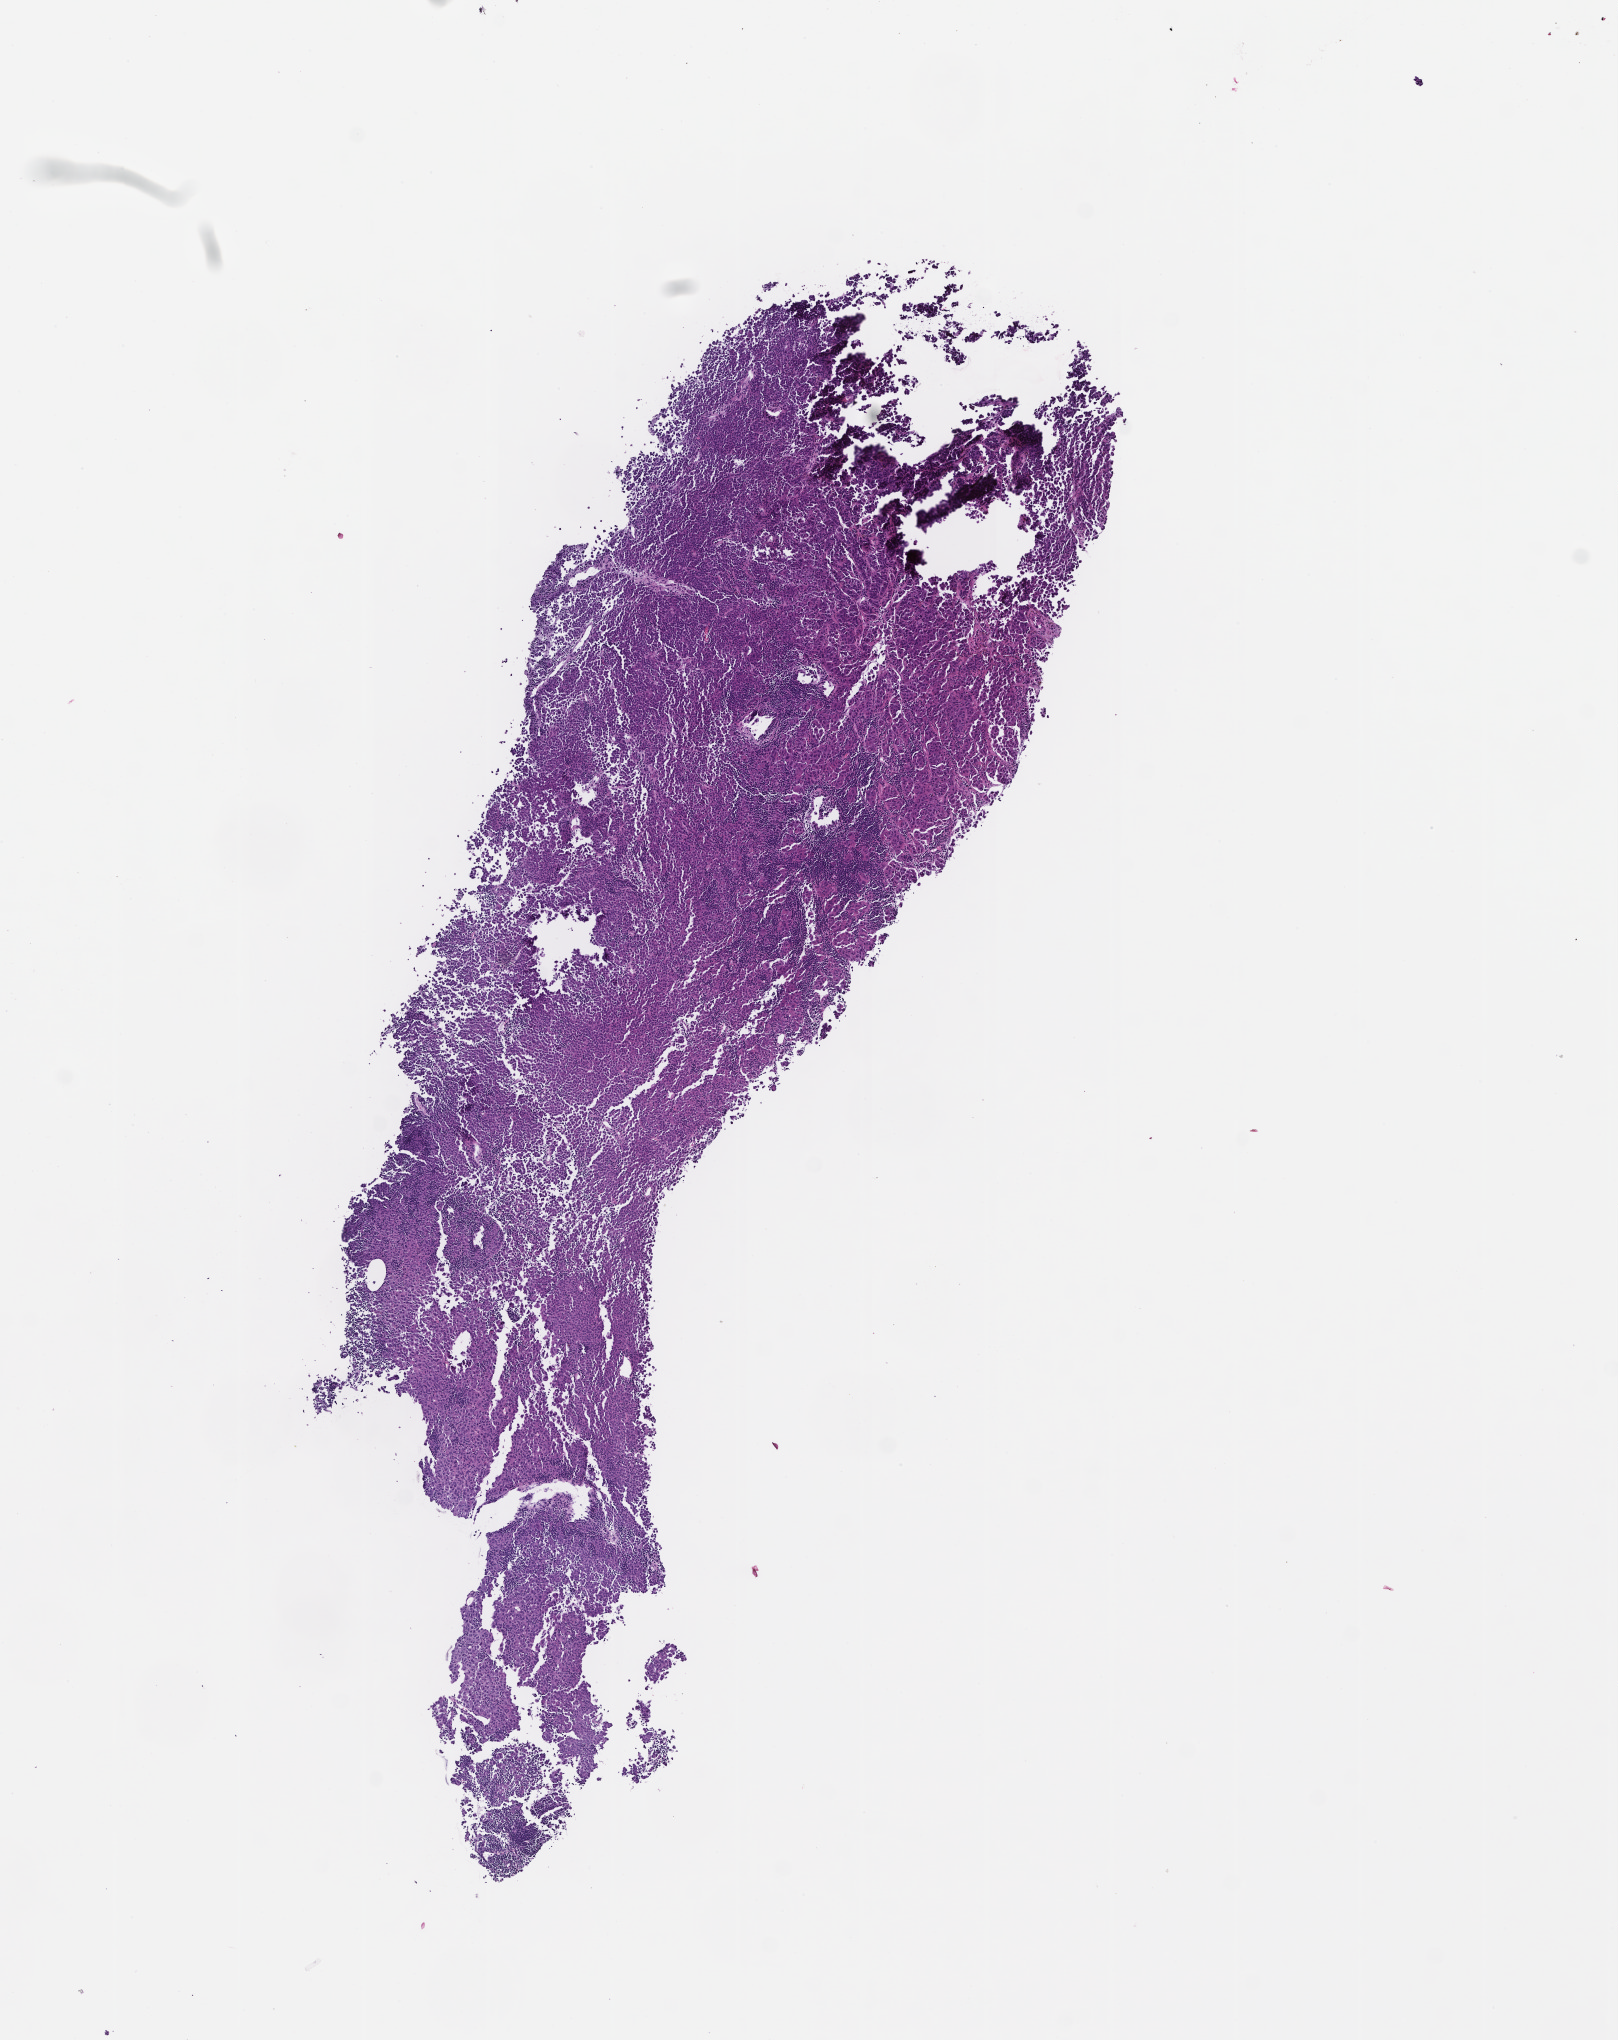
Haematoxylin and eosin whole-slide image, whole scanned area (about 6.5 x 8.2 mm) shown as a low-resolution overview. FFPE section. Patient: male.
* this section: metastatic tumor tissue
* patient diagnosis (primary): Melanoma